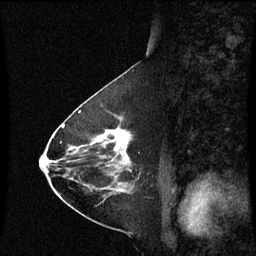
Breast MRI (dynamic contrast-enhanced), one sagittal slice; dynamic contrast-enhanced series, image 2 of 3 at this slice position (ordered by acquisition); 1.5 T; TE 4.2 ms, TR 8.9 ms; 2 mm slice thickness; 256 × 256 image matrix, field of view 200 × 200 mm. Female patient, age 63 years. From the clinical record (not read from this slice): setting: breast cancer imaged before/during neoadjuvant chemotherapy; receptor status: HR-positive, HER2-negative.
Annotated regions visible in this slice (semi-automatically segmented with operator editing):
- analysis volume of interest (the breast-tissue region the enhancement analysis was run in; not a lesion): bounding box [x1, y1, x2, y2] px = [94, 120, 142, 177]
- tumour enhancement mask (voxels above the 70 % enhancement threshold inside the analysis volume of interest): [107, 132, 130, 161]